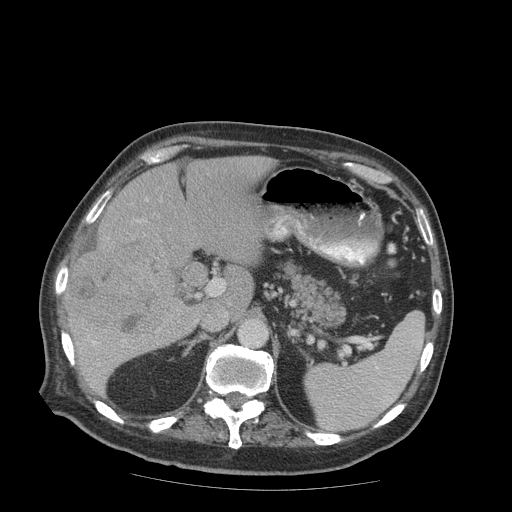
Contrast-enhanced abdominal CT (liver protocol), one axial slice; slice 50 of 99 in the series (ordered by position); reconstruction kernel STANDARD; 140 kVp; soft-tissue window (W 400 / L 40 HU); 2.5 mm slice thickness; 512 × 512 image matrix, field of view 420 × 420 mm. Case-level facts recorded for this patient, not image findings: diagnosis: hepatocellular carcinoma (patient treated with transarterial chemoembolisation; whether this scan precedes or follows treatment is not stated here); TNM stage (as recorded): Stage-IIIB; Child-Pugh class: A; tumour nodularity: multinodular.
Annotated regions visible in this slice (semi-automatic segmentation, software-assisted and operator-edited):
- liver parenchyma outside the tumour (the mass and vessels are separate outlines, so this box may not span the whole liver): box from (x=66, y=156) to (x=276, y=393) px
- mass: (x=63, y=243)–(x=174, y=341)
- liver vessels: (x=92, y=221)–(x=139, y=345)